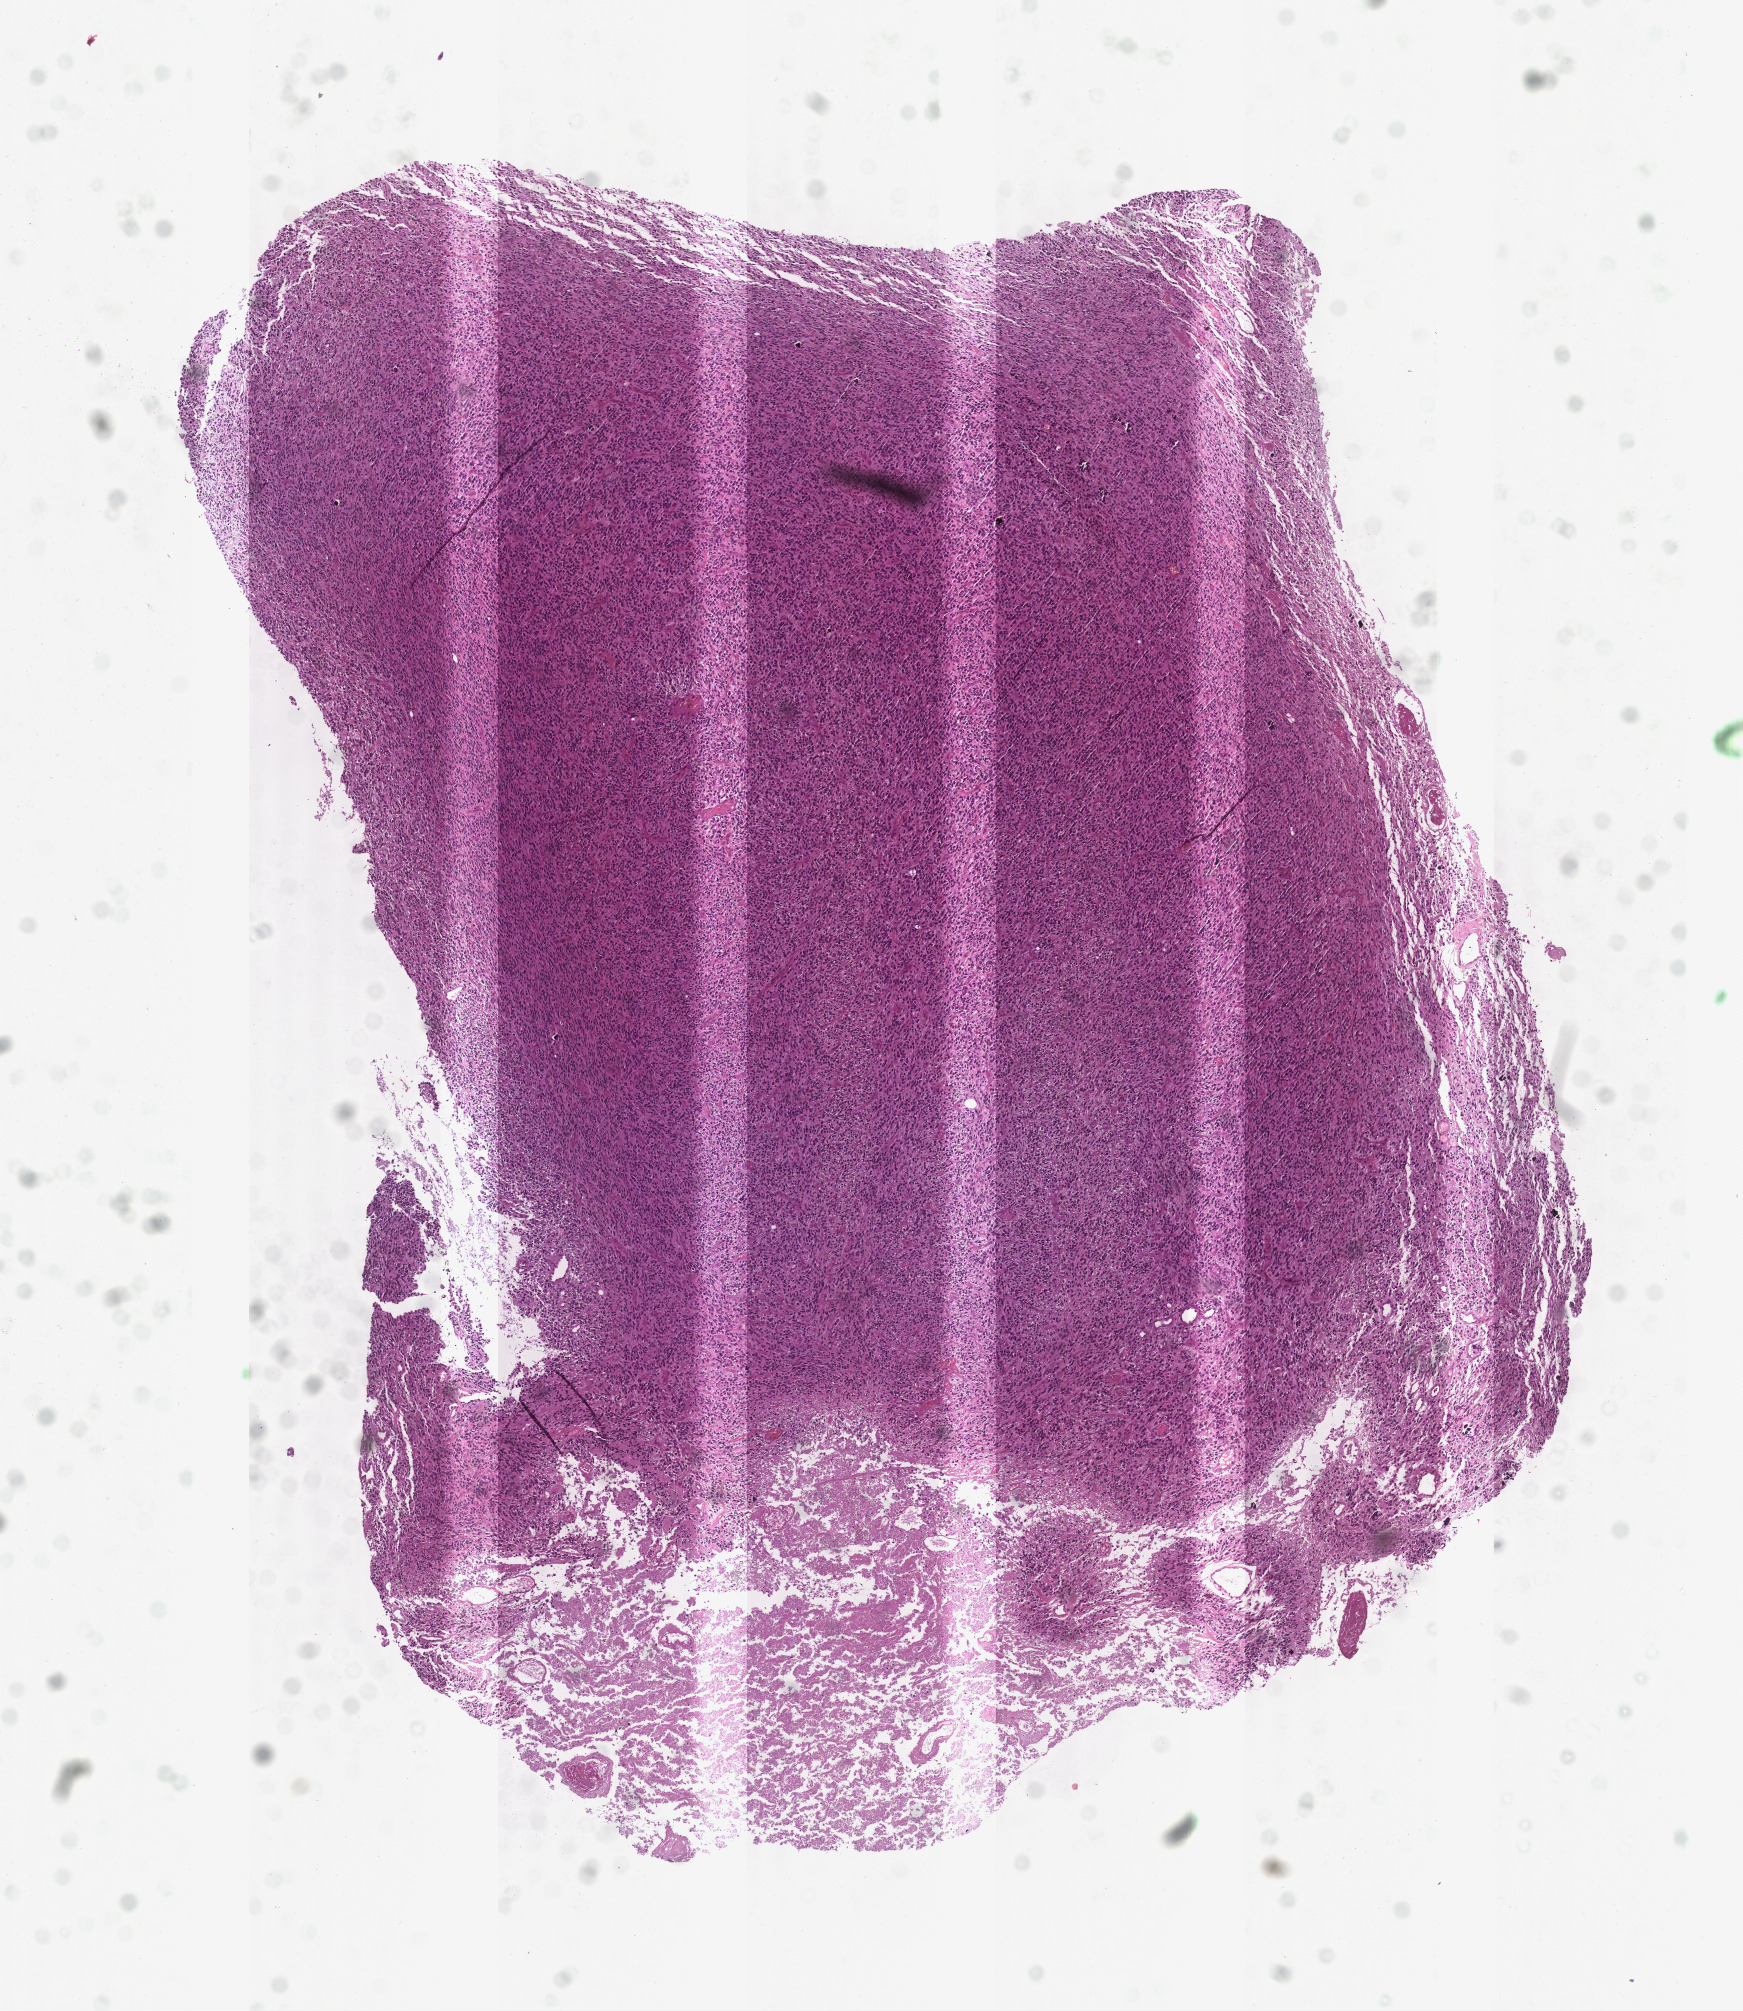
Whole-slide histology image, H&E-stained — shown as a low-resolution overview of the whole scanned area (about 7.0 x 8.1 mm). Tumour tissue sample, brain. Male, 44 y/o.
• histologic diagnosis: Glioblastoma